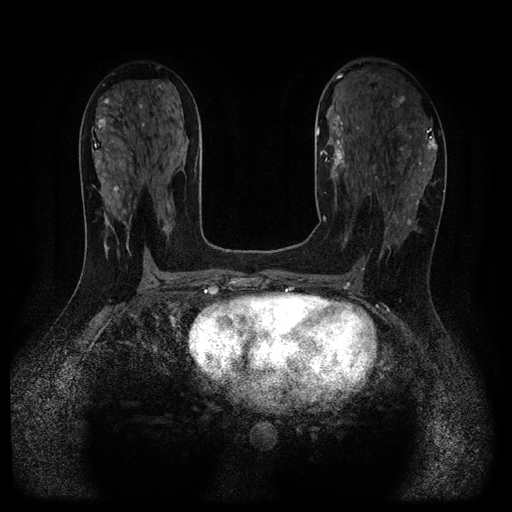
Breast MRI (dynamic contrast-enhanced, multi-phase), one axial slice. Position 57 of 116 along the scan axis. Dynamic contrast-enhanced series, time point 2 of 5 at this slice position (early post-contrast). 1.5 T. TE 2.7 ms, TR 5.4 ms. 2.2 mm slice thickness. 512 × 512 image matrix, field of view 330 × 330 mm. Female patient, age 43 years.
Structures marked on this image (semi-automatically segmented with operator editing):
- breast lesion (labelled benign in the annotation): bounding box <320,115,350,188> (left, top, right, bottom; pixels)